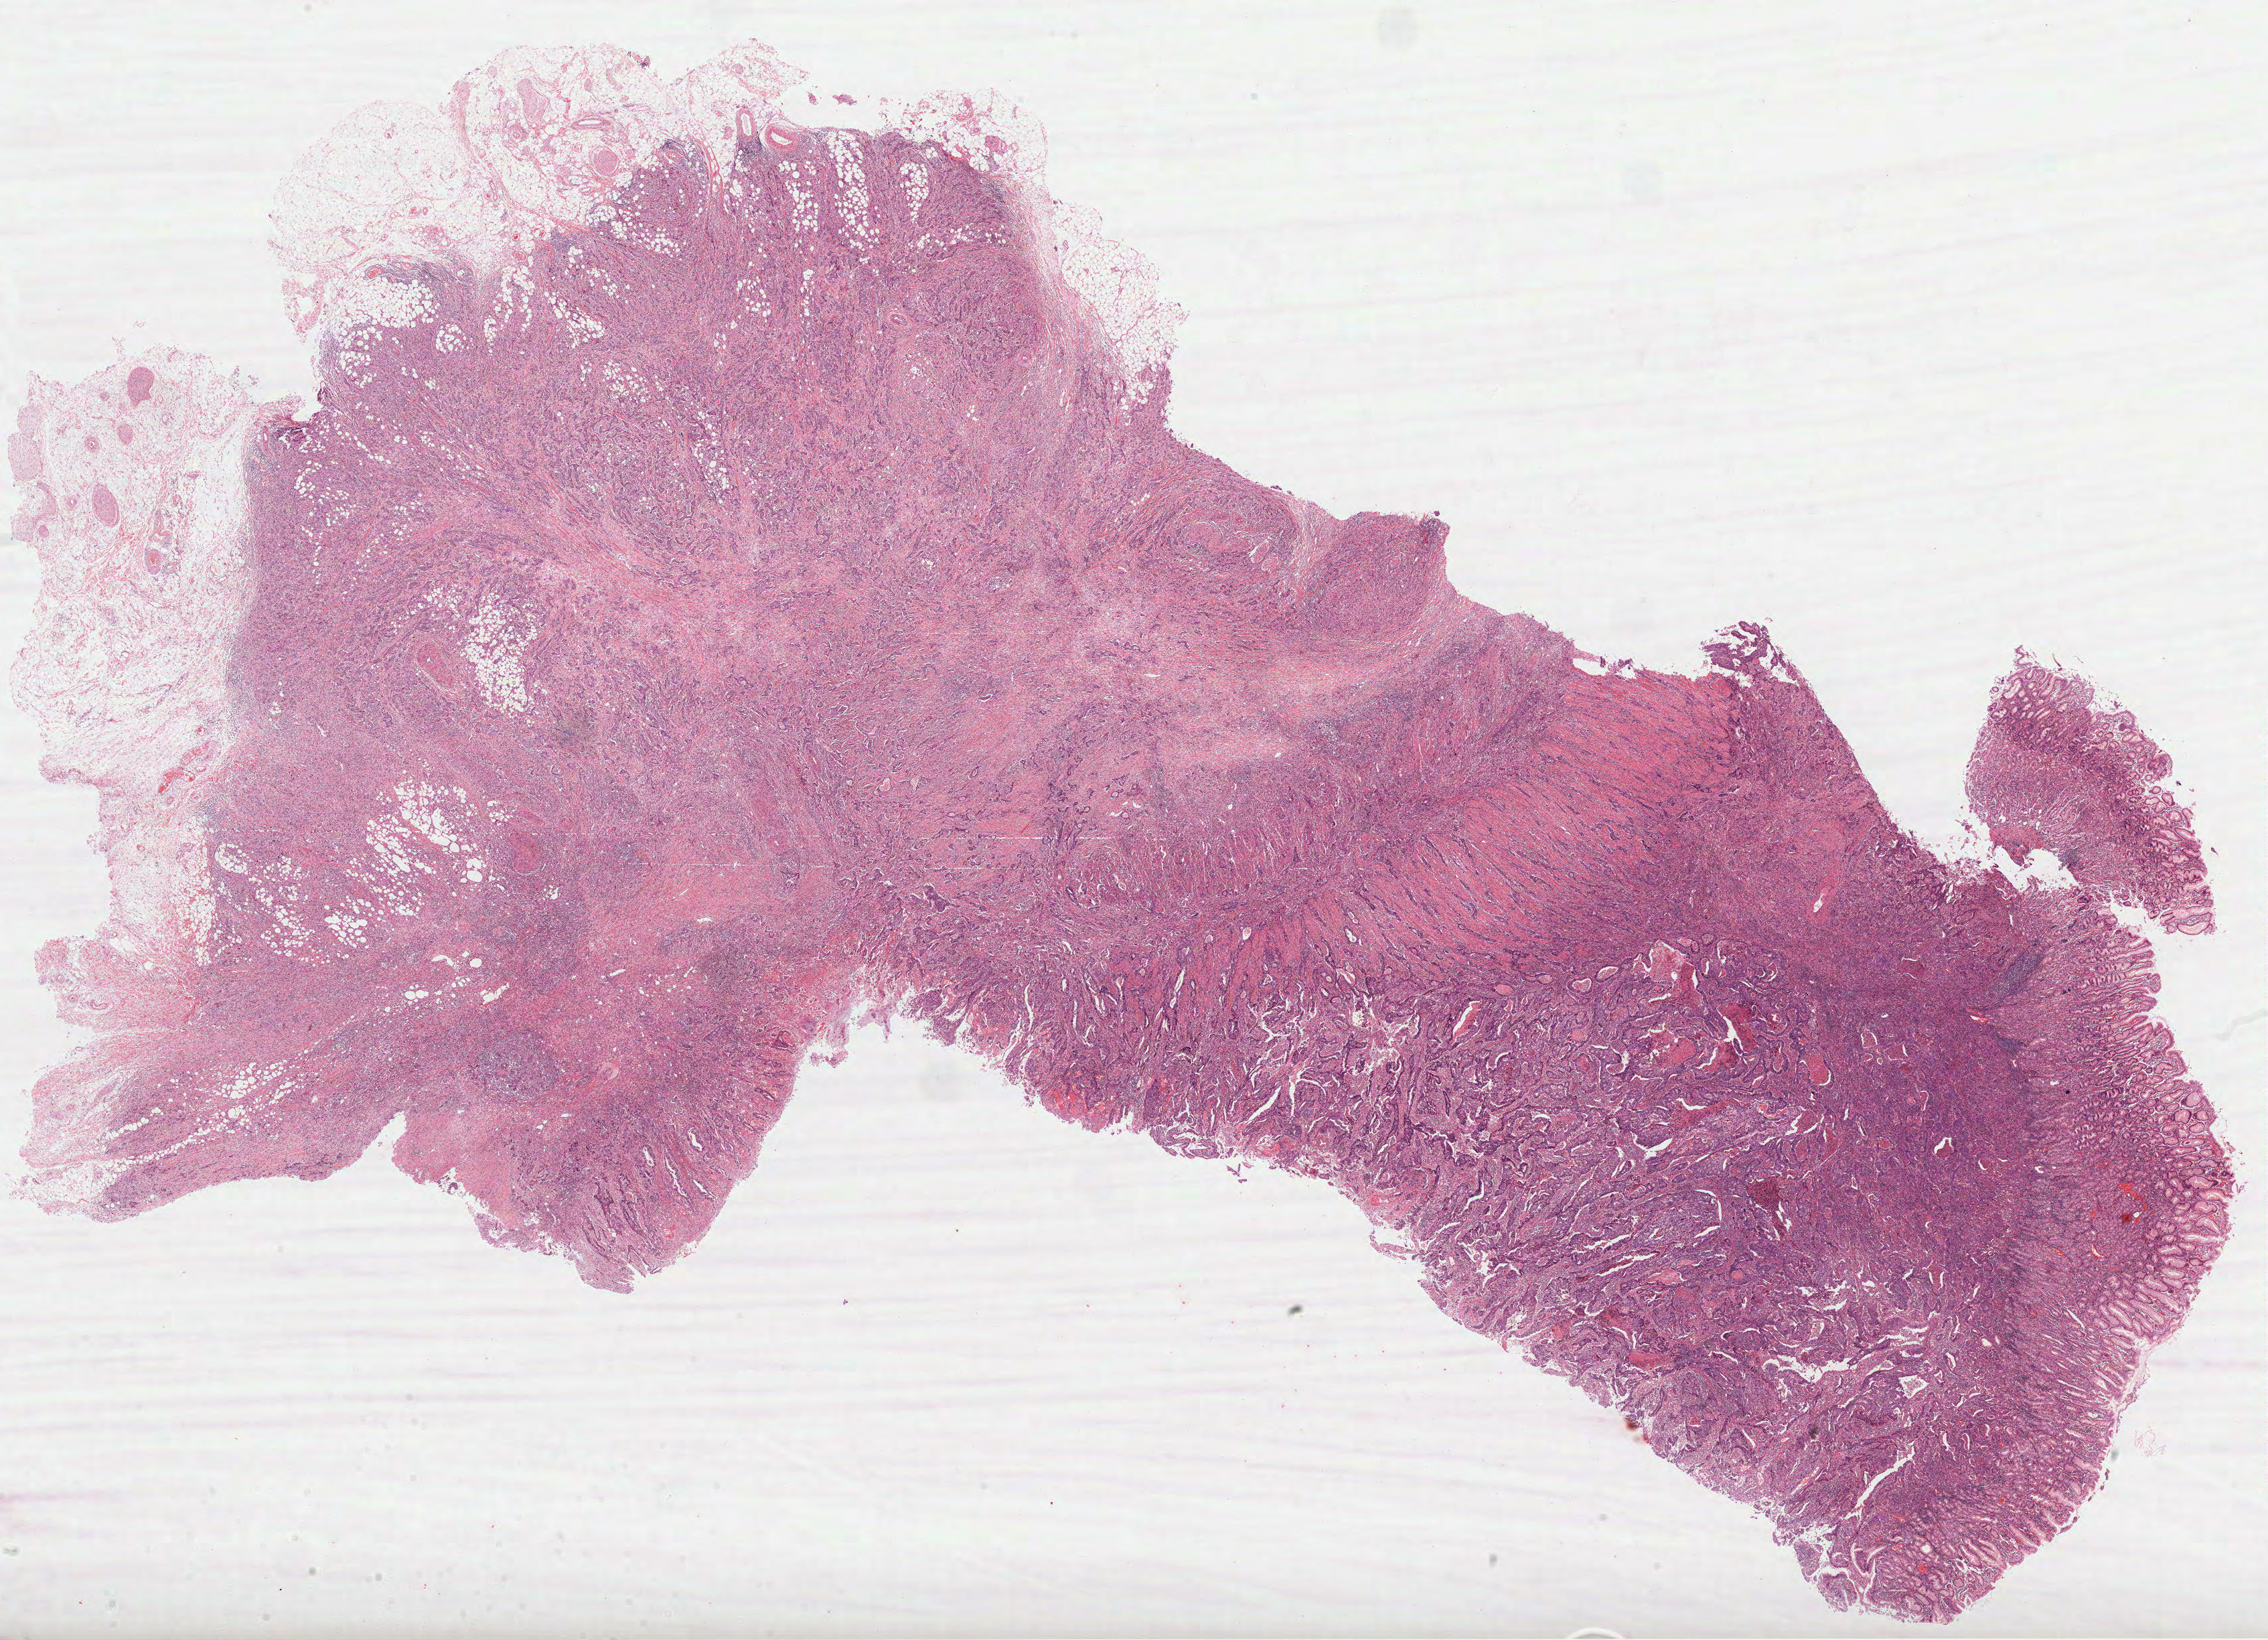
H&E whole-slide image, low-resolution overview of the scanned area, about 27.3 x 19.8 mm (slide scanned at 40x), formalin-fixed paraffin-embedded (FFPE) diagnostic section, stomach, primary tumour sample. Patient: female, age at initial diagnosis 54 years. Histologic grade: G2 (moderately differentiated).
Lymph nodes positive (case pathology): 10 of 10 examined. Pathologic diagnosis: Adenocarcinoma, NOS (cardia, NOS). AJCC pathologic stage: IIIB.